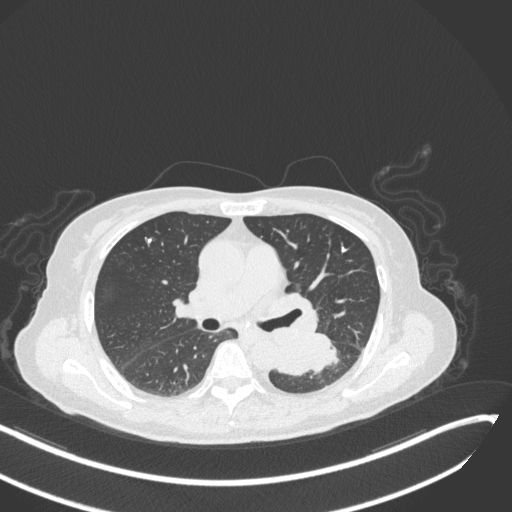
Chest CT, one axial slice. Slice 162 of 342 in the series (ordered by position). Reconstruction kernel B31f. 120 kVp. Lung window (W 1500 / L -600 HU). 512 × 512 image matrix, field of view 400 × 400 mm. Patient: female, 64 years. Case-level facts recorded for this patient, not image findings: clinical TNM (as recorded): T3 N1 M1; histopathological grade: G3.
Annotated regions visible in this slice (bounding box drawn by a radiologist):
- lung tumour (recorded histology: small cell carcinoma): bounding box [x1, y1, x2, y2] px = [276, 330, 340, 378]